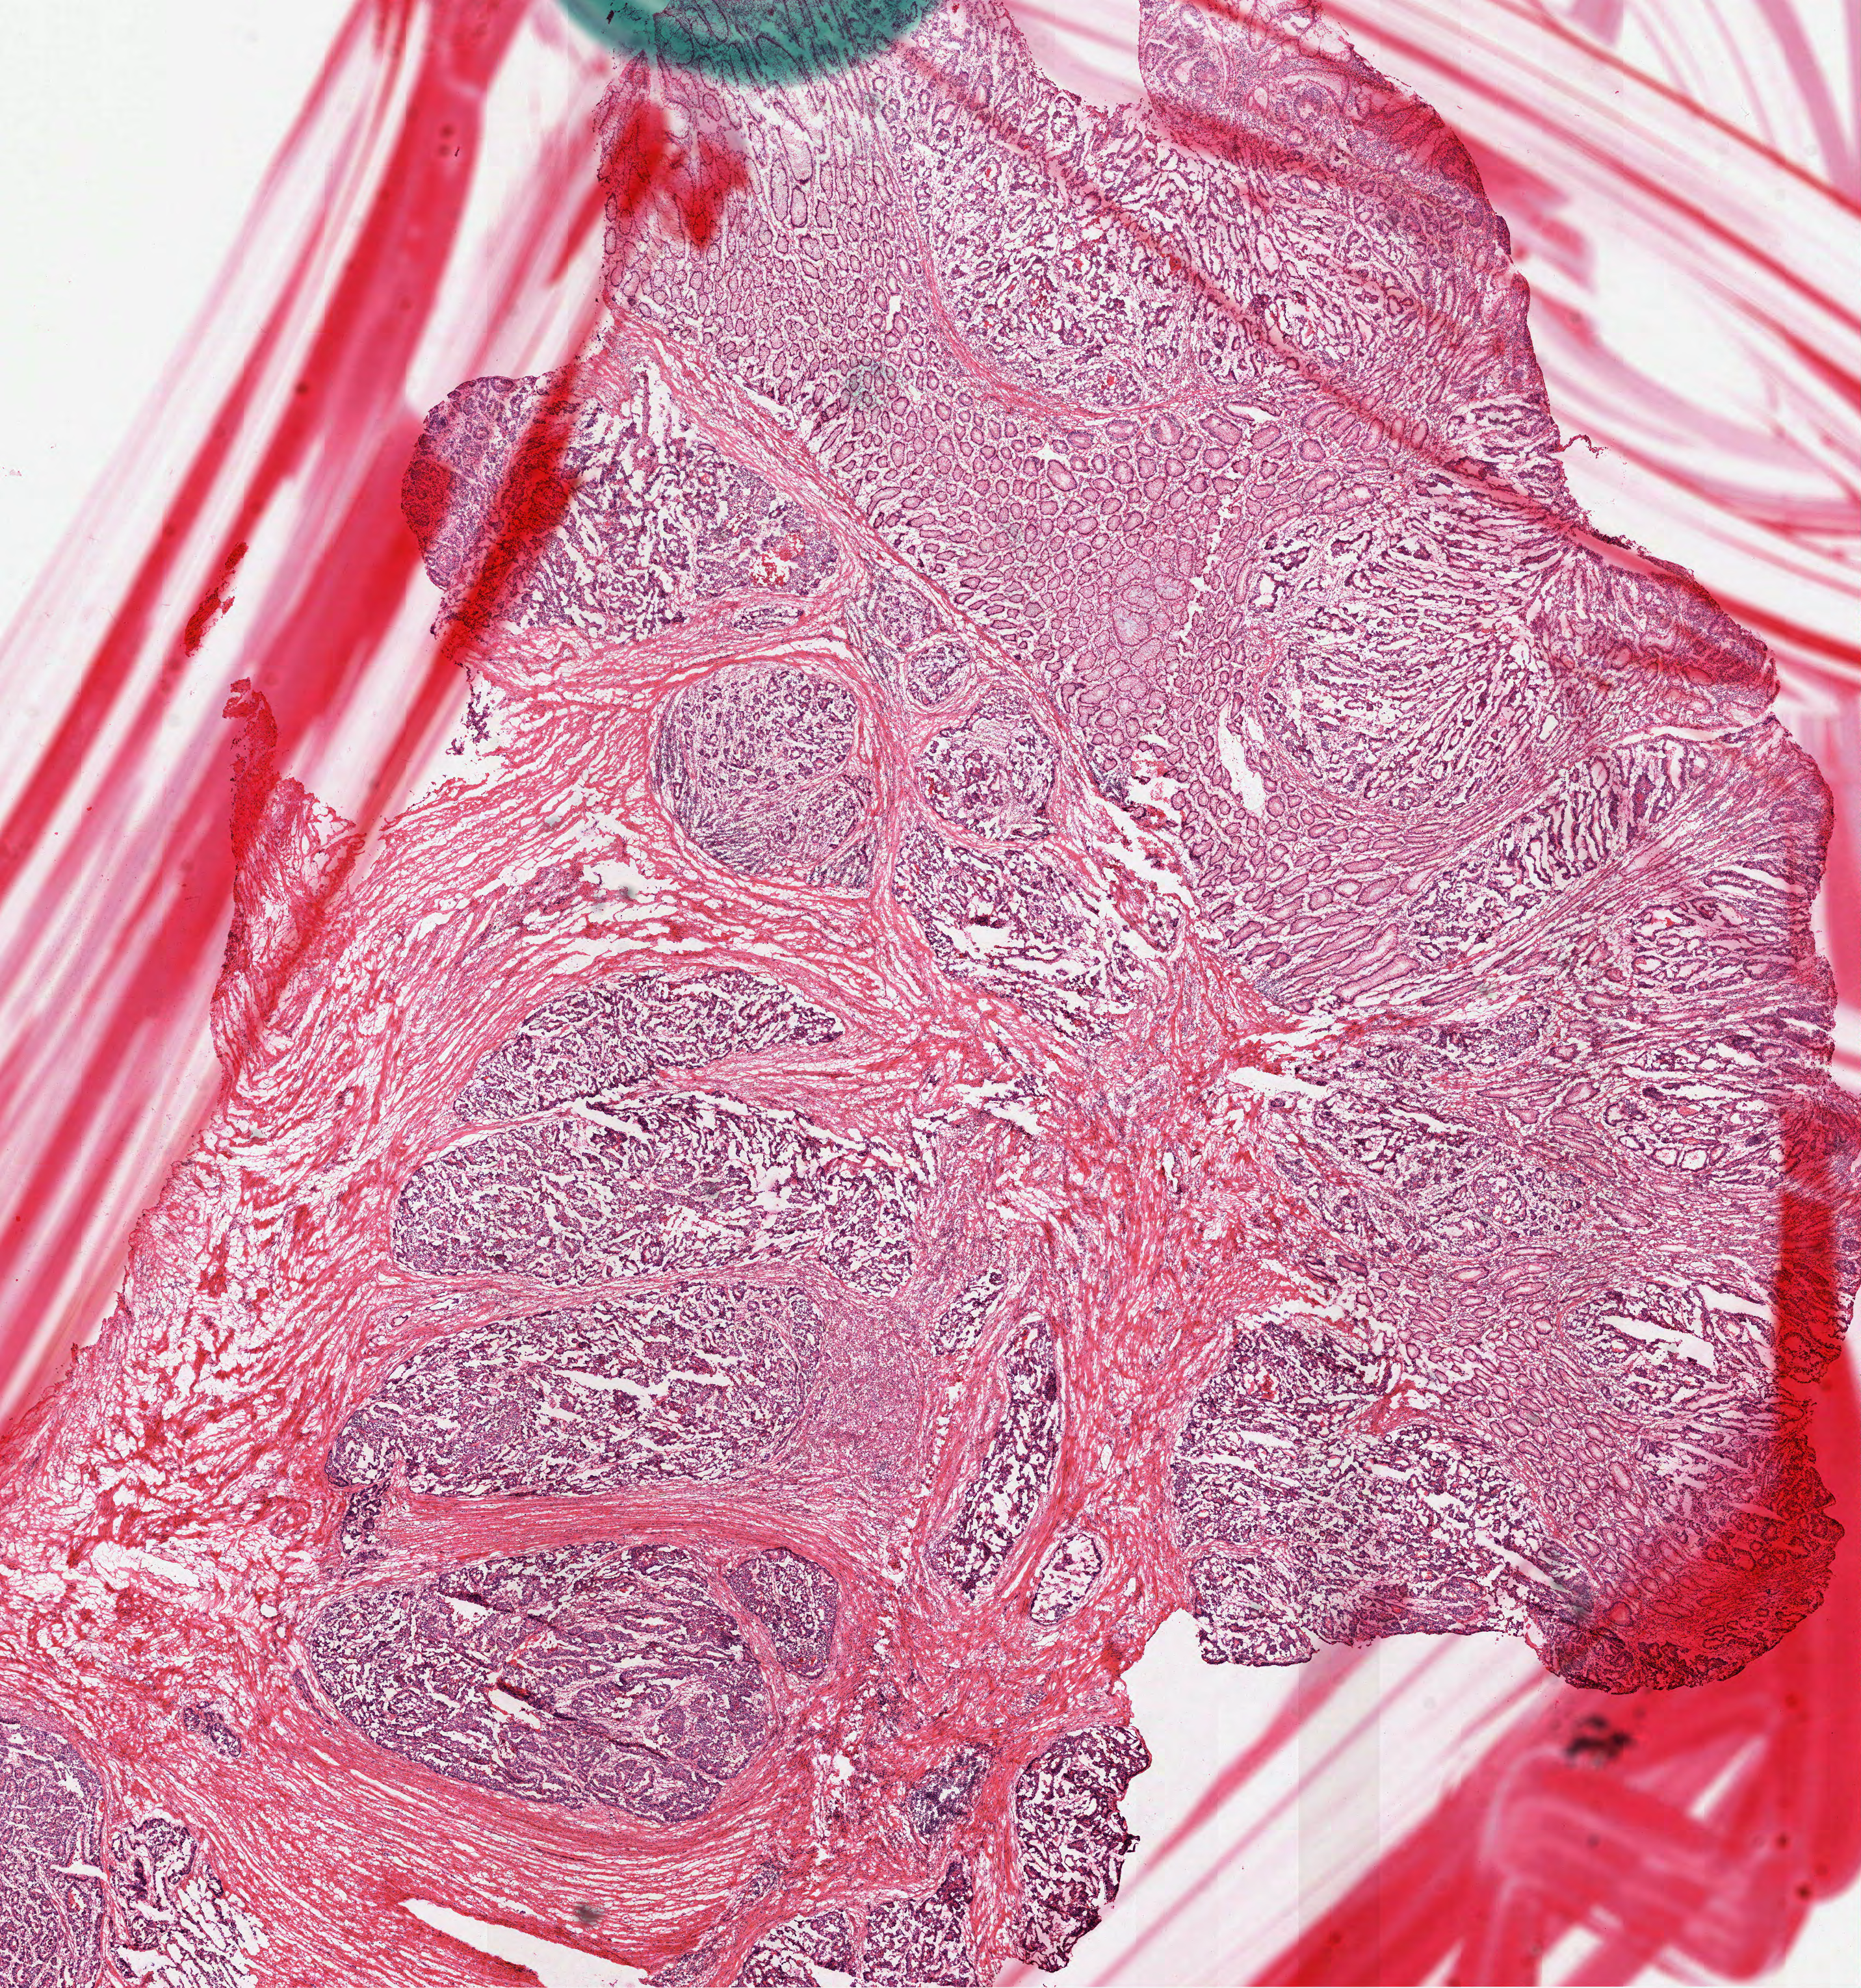
H&E-stained whole-slide image — a low-resolution overview of the entire scanned area, about 11.5 x 12.3 mm (acquisition: 40x scan), frozen section from the top of the tissue portion, colon, primary tumour sample. Patient: female, age at initial diagnosis 51 years. Slide review estimates, as recorded: tumour cells 85%, tumour nuclei 71%, normal cells 14%, stromal cells 0%, necrosis 1%. Infiltration values recorded for this section: lymphocyte infiltration 5%, monocyte infiltration 0%, neutrophil infiltration 2%.
* lymph nodes positive (case pathology): 1 of 6 examined
* AJCC pathologic stage: IIIB
* diagnosis: Adenocarcinoma, NOS (sigmoid colon)